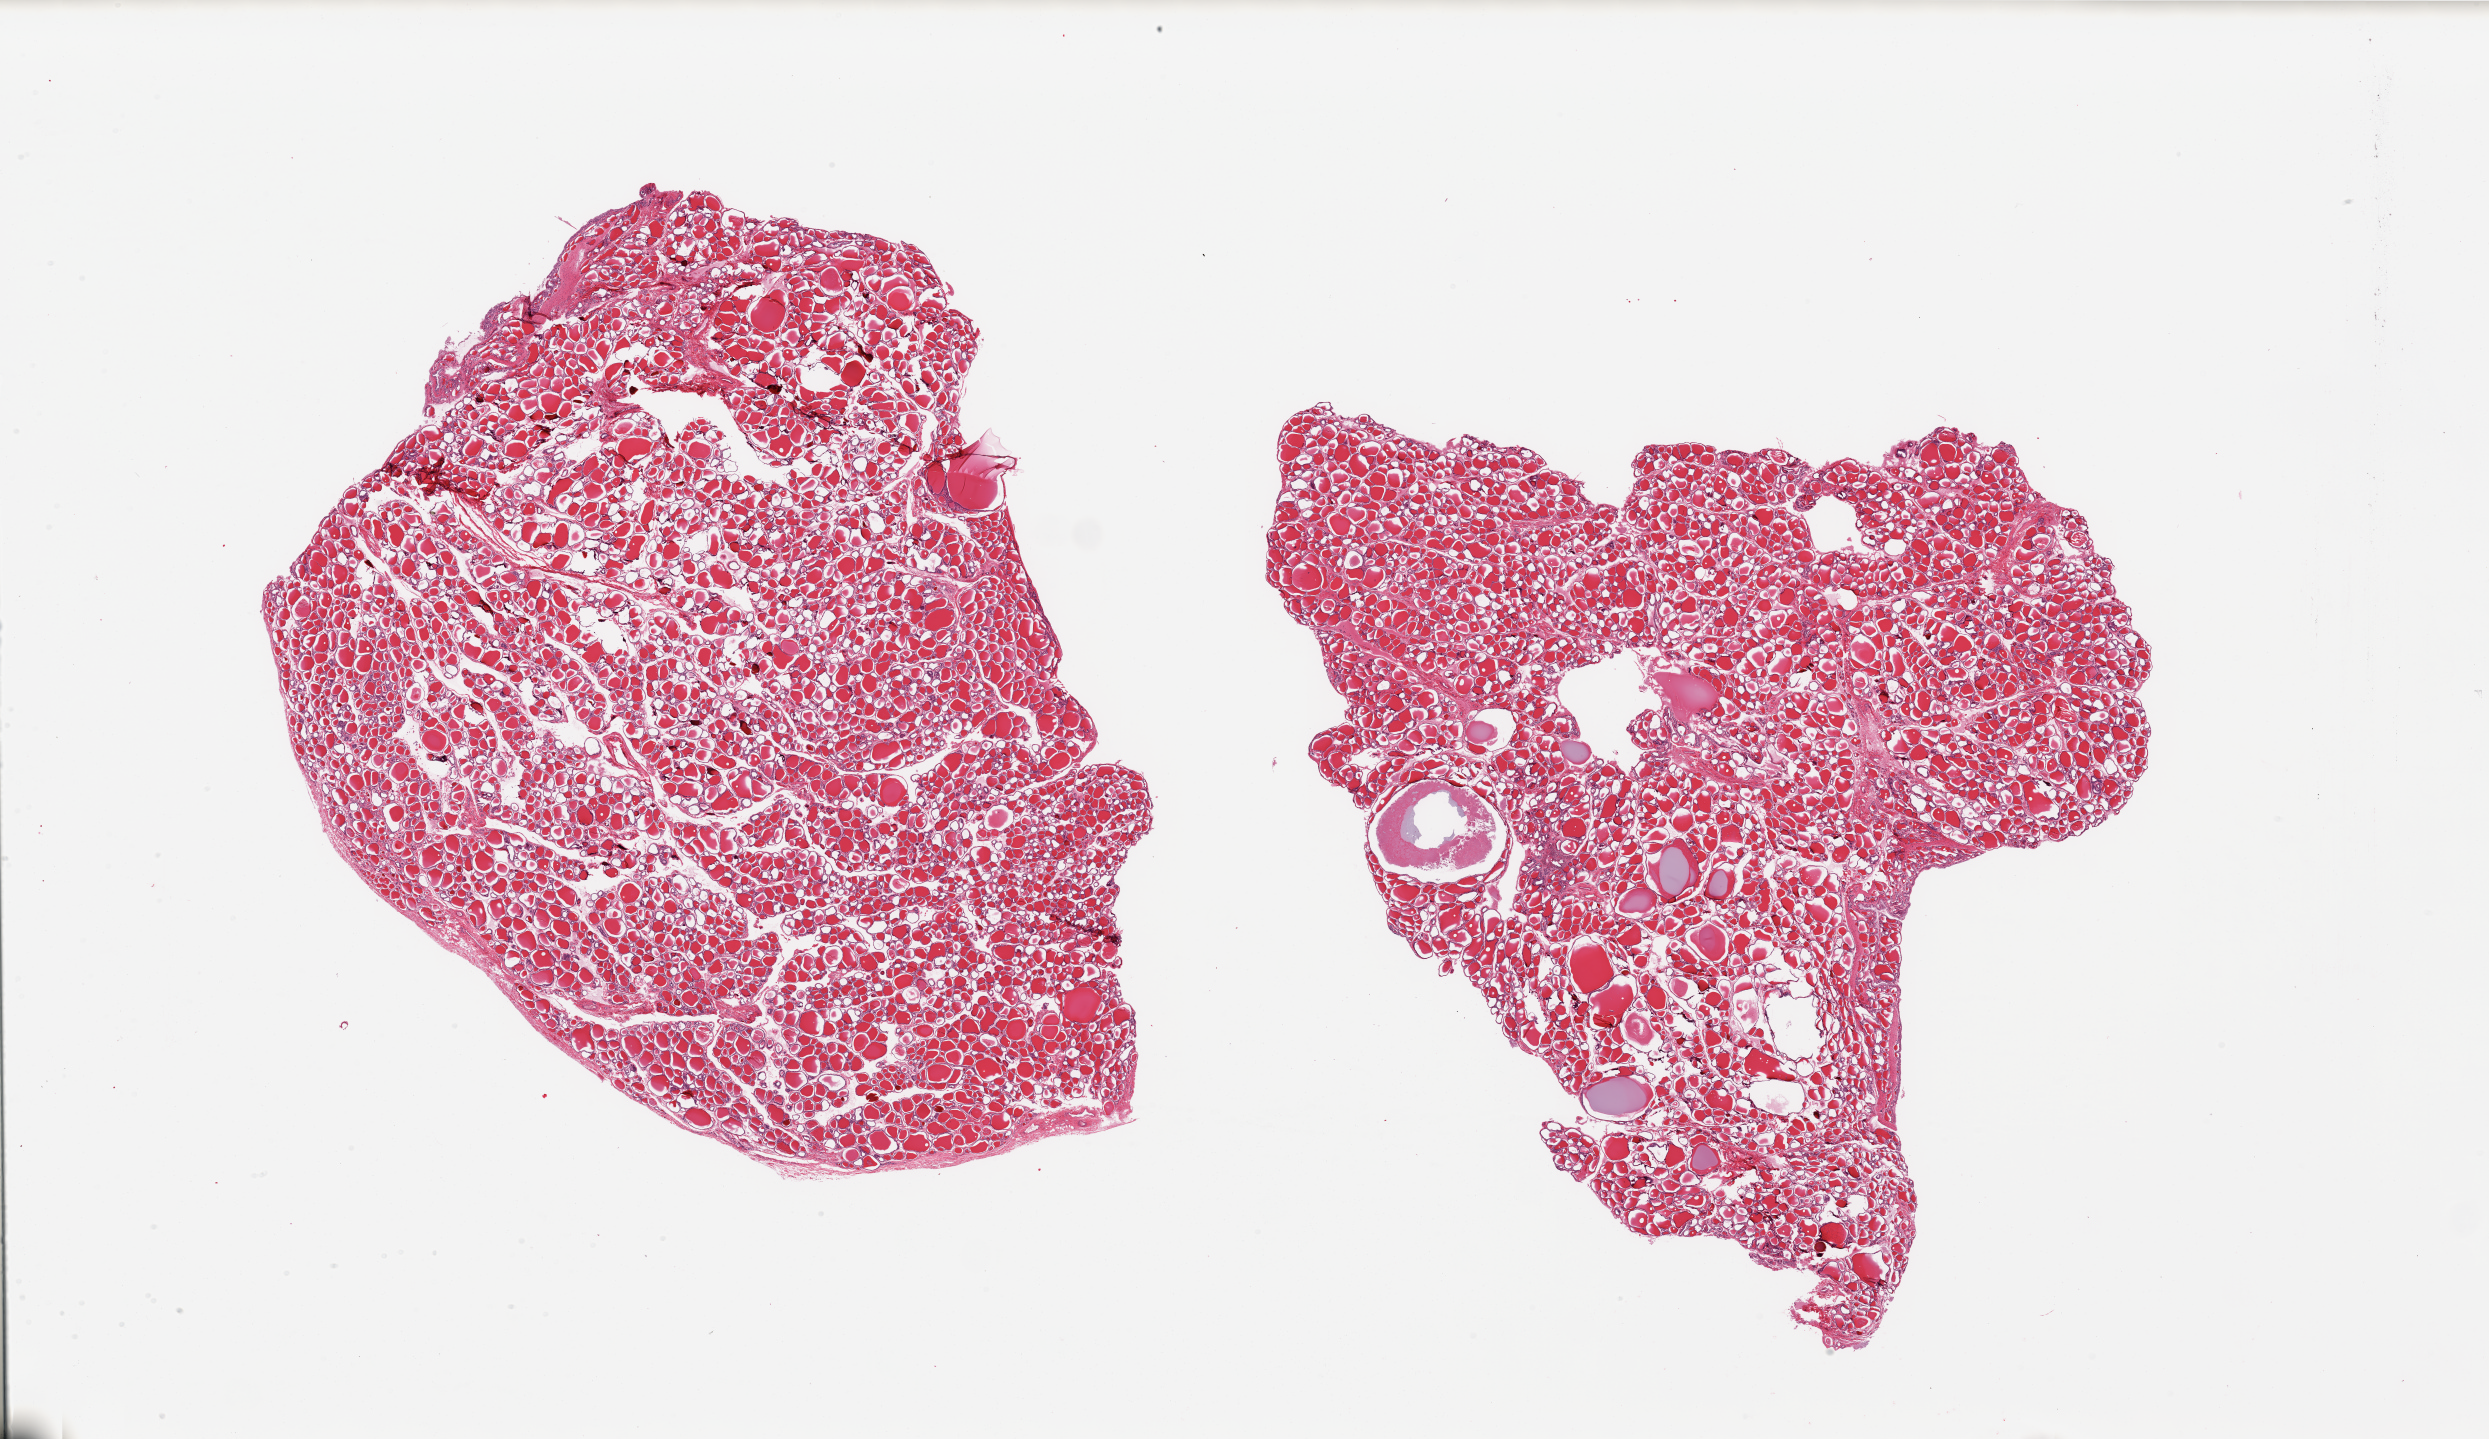
Haematoxylin and eosin whole-slide image, a low-resolution overview of the entire scanned area, about 39.4 x 22.8 mm; PAXgene-fixed, paraffin-embedded tissue; section of thyroid (target tissue); tissue donor sample. Female donor.
Pathologist's review note for this sample: 2 pieces; nodularity with few colloid cysts.